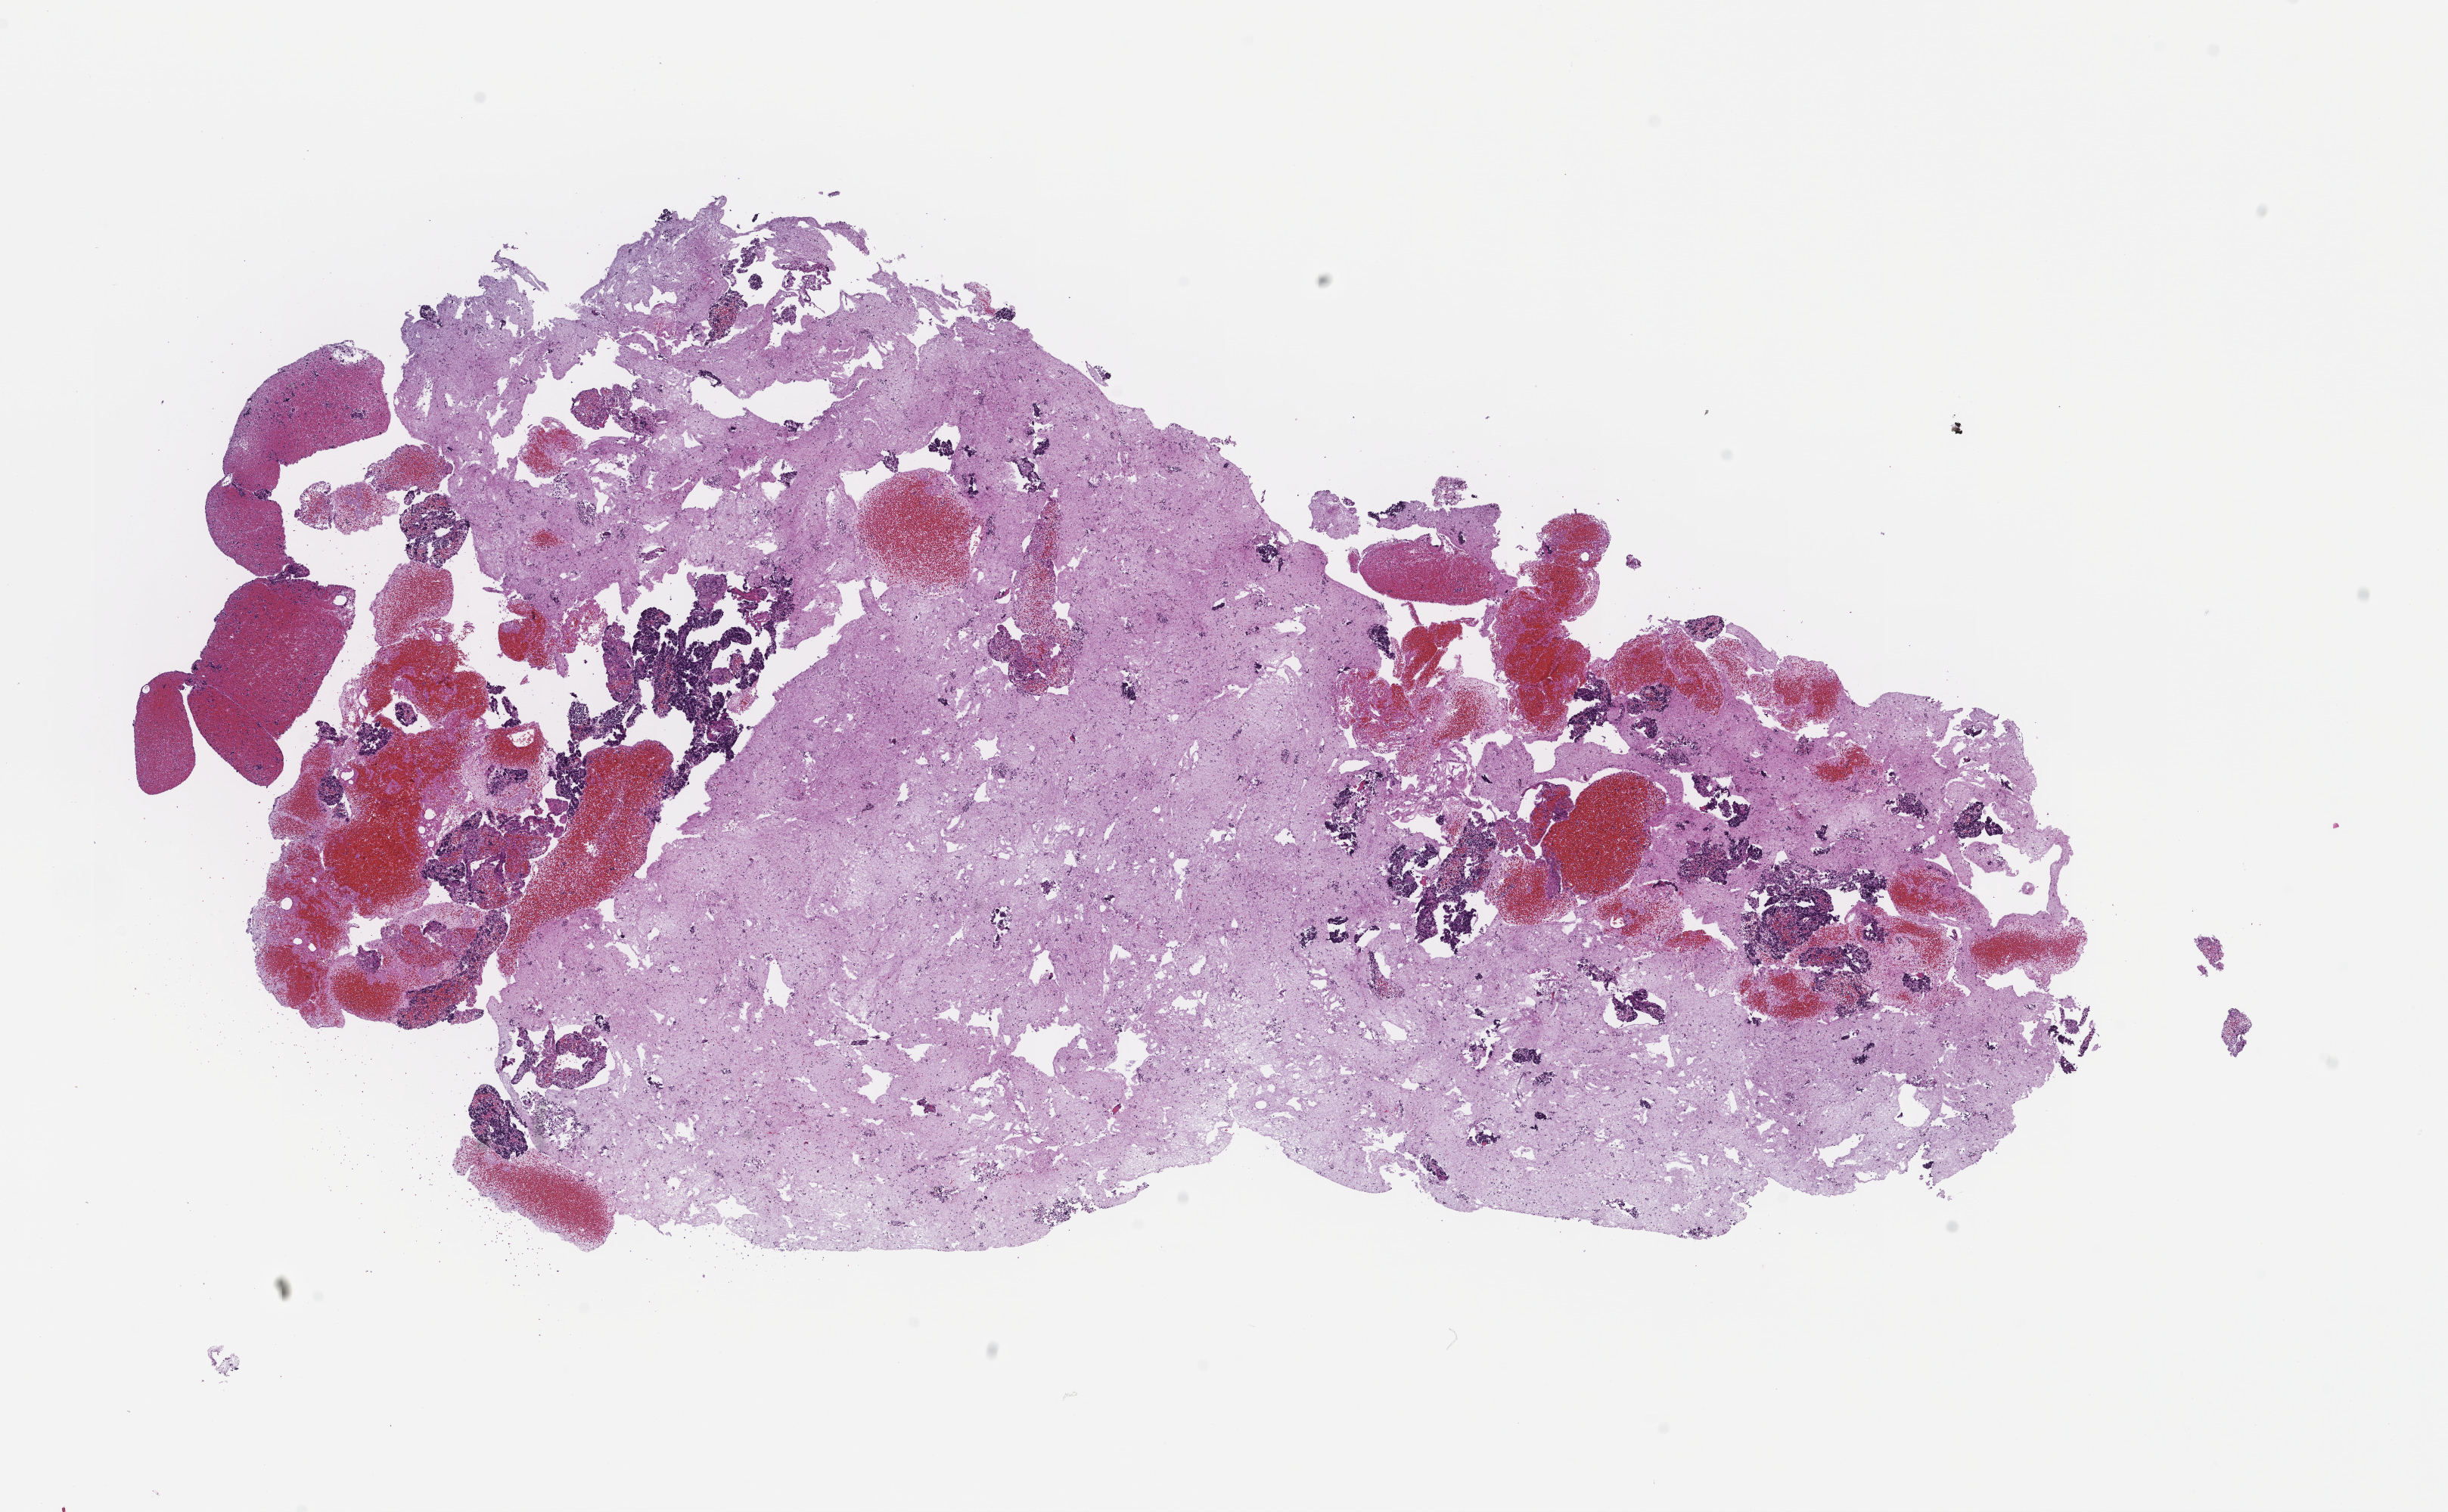
Digitized H&E-stained section — whole scanned area (about 13.1 x 8.1 mm) shown as a low-resolution overview; formalin-fixed paraffin-embedded section; site: lung. Male patient.
This section: primary tumour tissue. Diagnosis: Small Cell Lung Carcinoma.